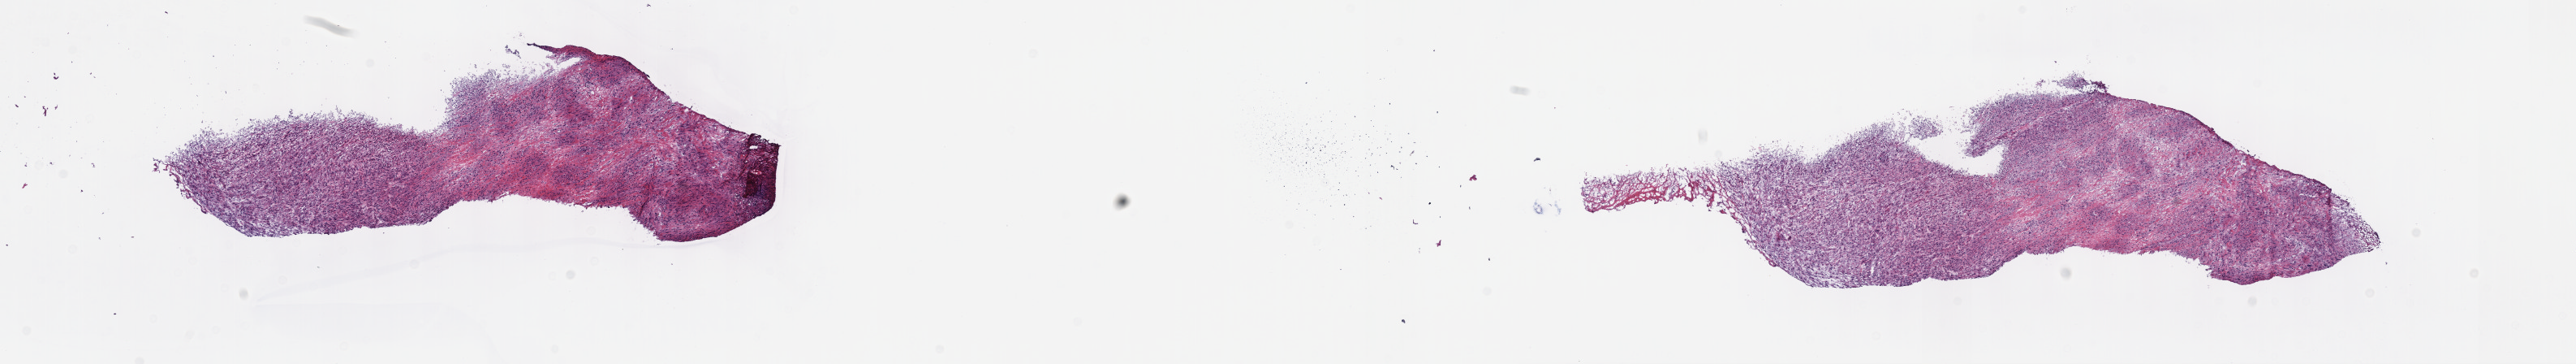
H&E-stained whole-slide image, shown as a low-resolution overview of the whole scanned area (about 25.7 x 3.6 mm, acquisition: 40x scan); frozen section from the top of the tissue portion; sample: primary tumour, stomach. Patient: female, age at initial diagnosis 58 years. Slide review estimates, as recorded: tumour cells 80%, tumour nuclei 95%, normal cells 0%, stromal cells 0%, necrosis 20%. Inflammatory infiltration, as recorded: lymphocyte infiltration 0%, monocyte infiltration 0%, neutrophil infiltration 0%.
- pathologic diagnosis: Leiomyosarcoma, NOS